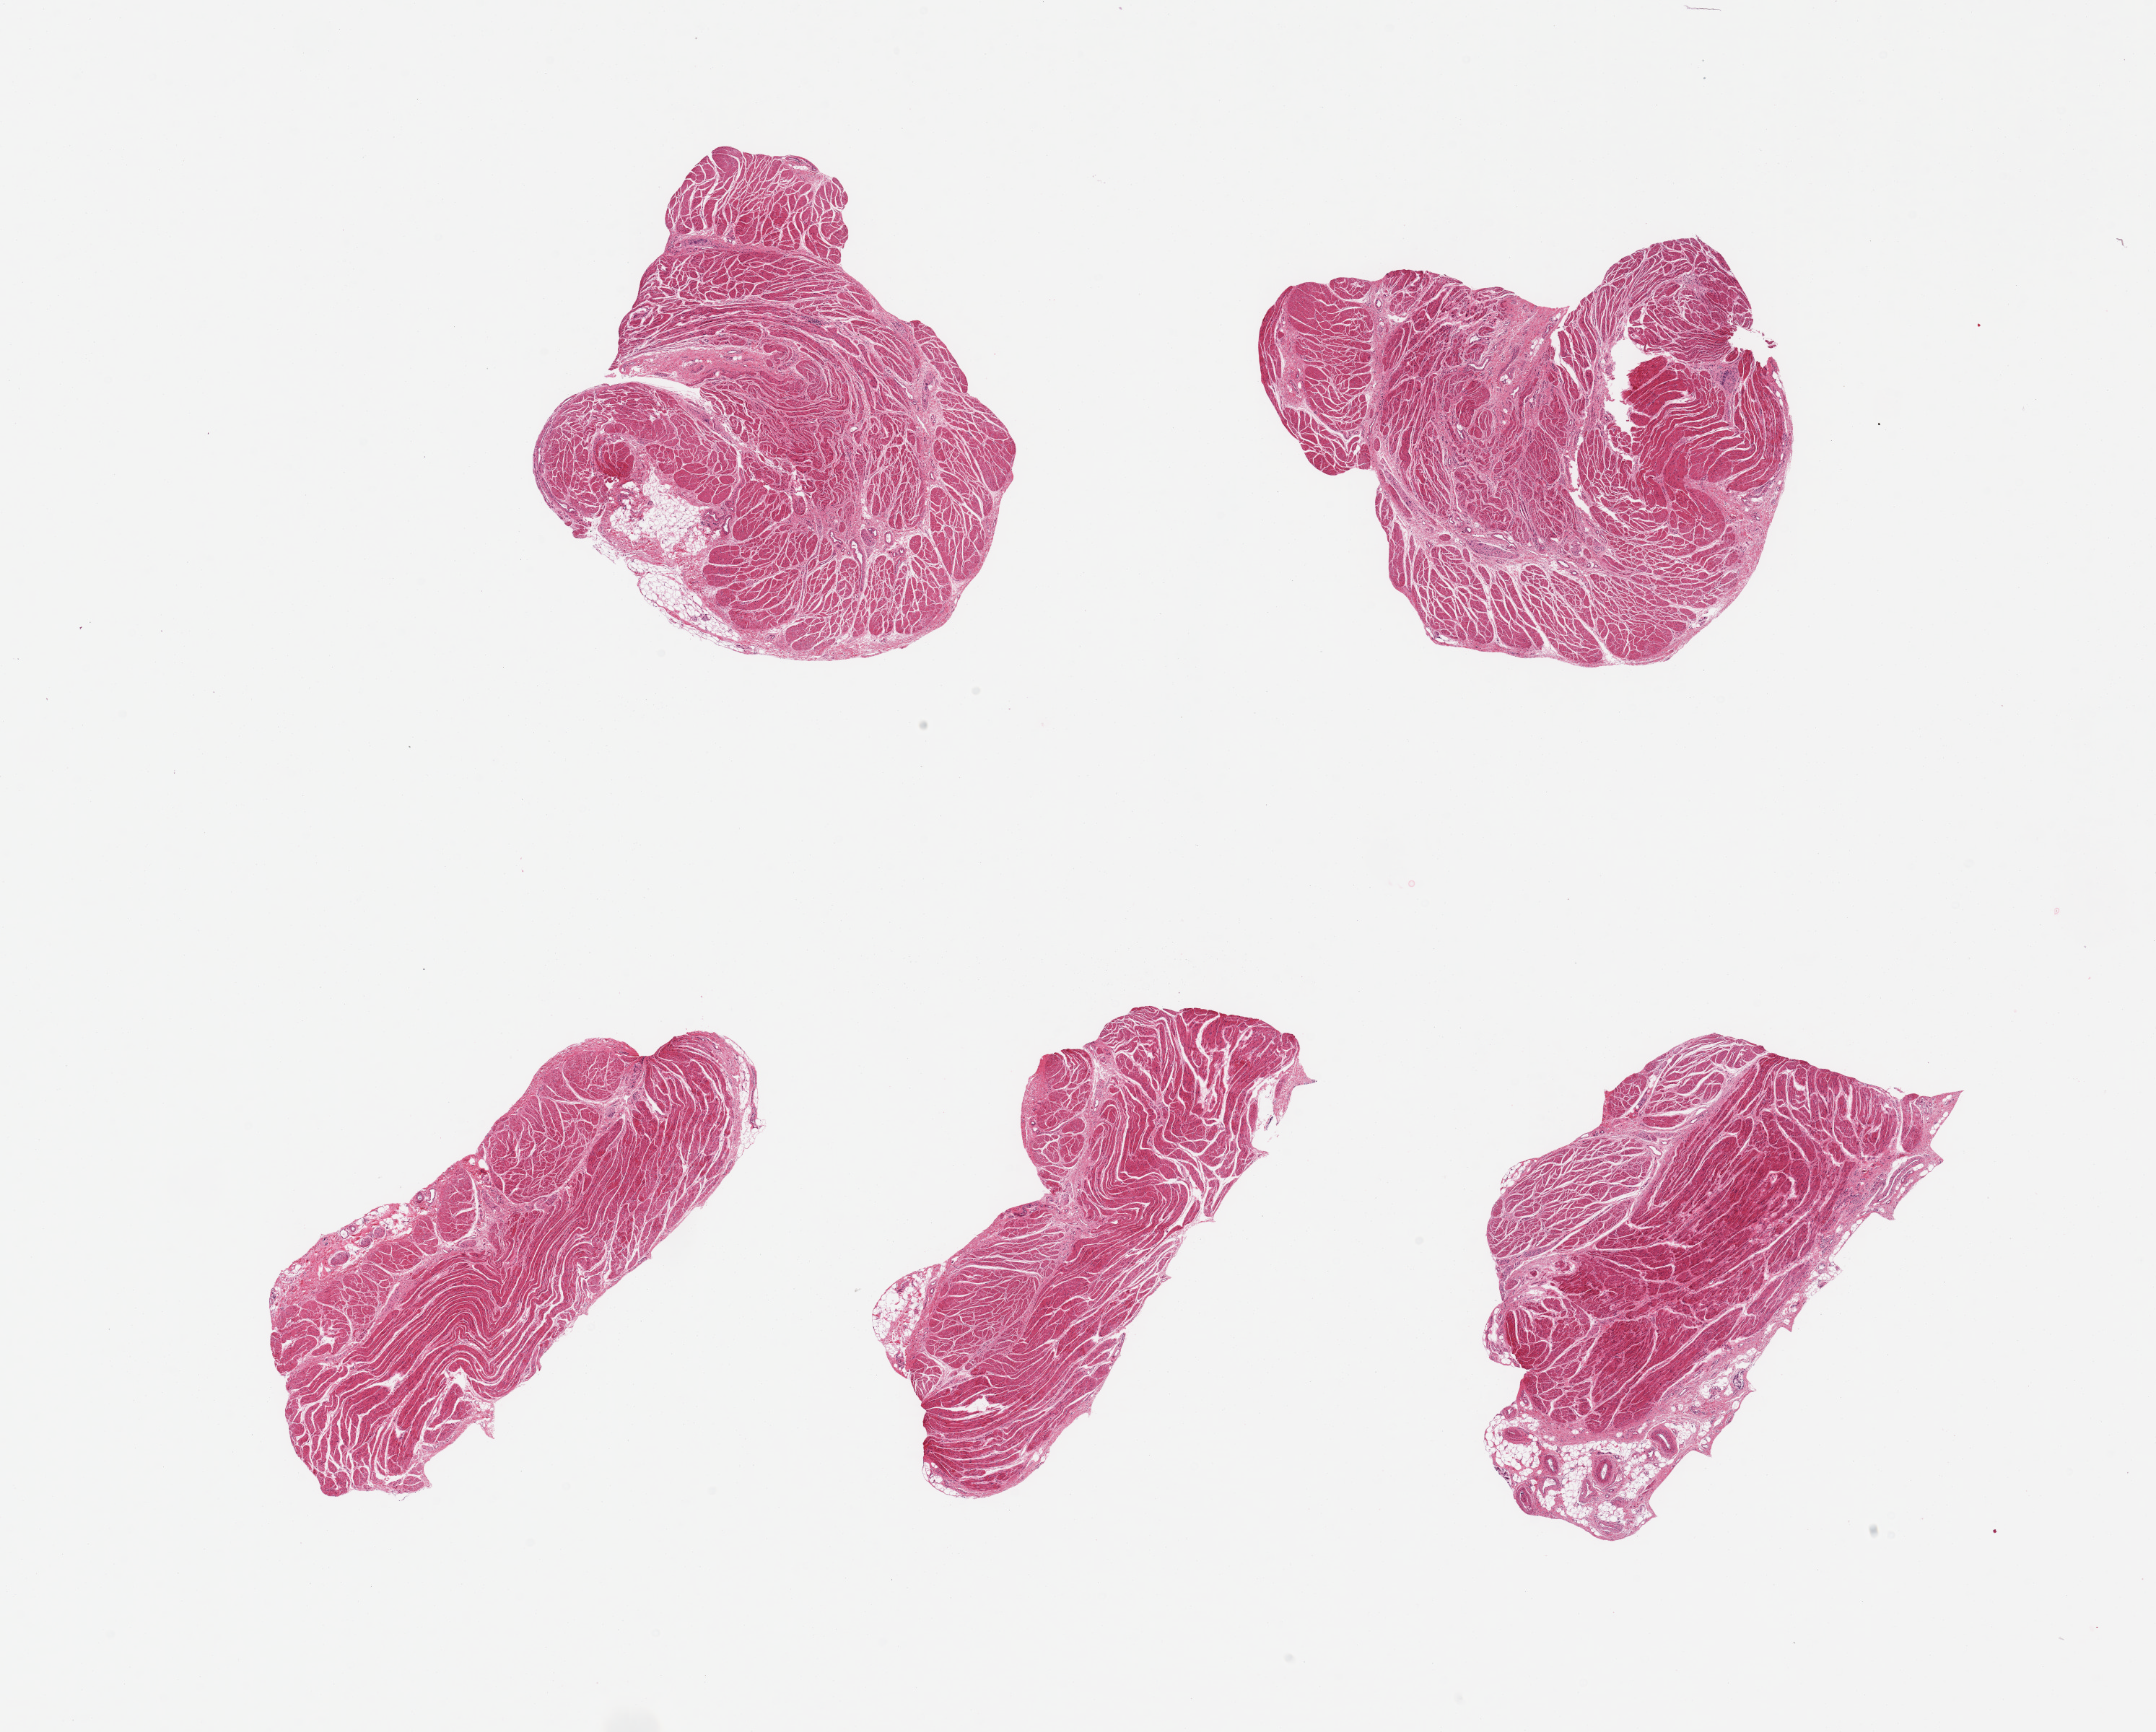
Haematoxylin and eosin whole-slide image — a low-resolution overview of the entire scanned area, about 23.6 x 19.0 mm, PAXgene-fixed paraffin-embedded (PFPE) section, sampled site (target tissue): gastroesophageal junction, donor tissue sample. Donor: male.
Reviewer comment on this tissue sample: 5 pieces; 2 have 10 & 20% stromal contents.